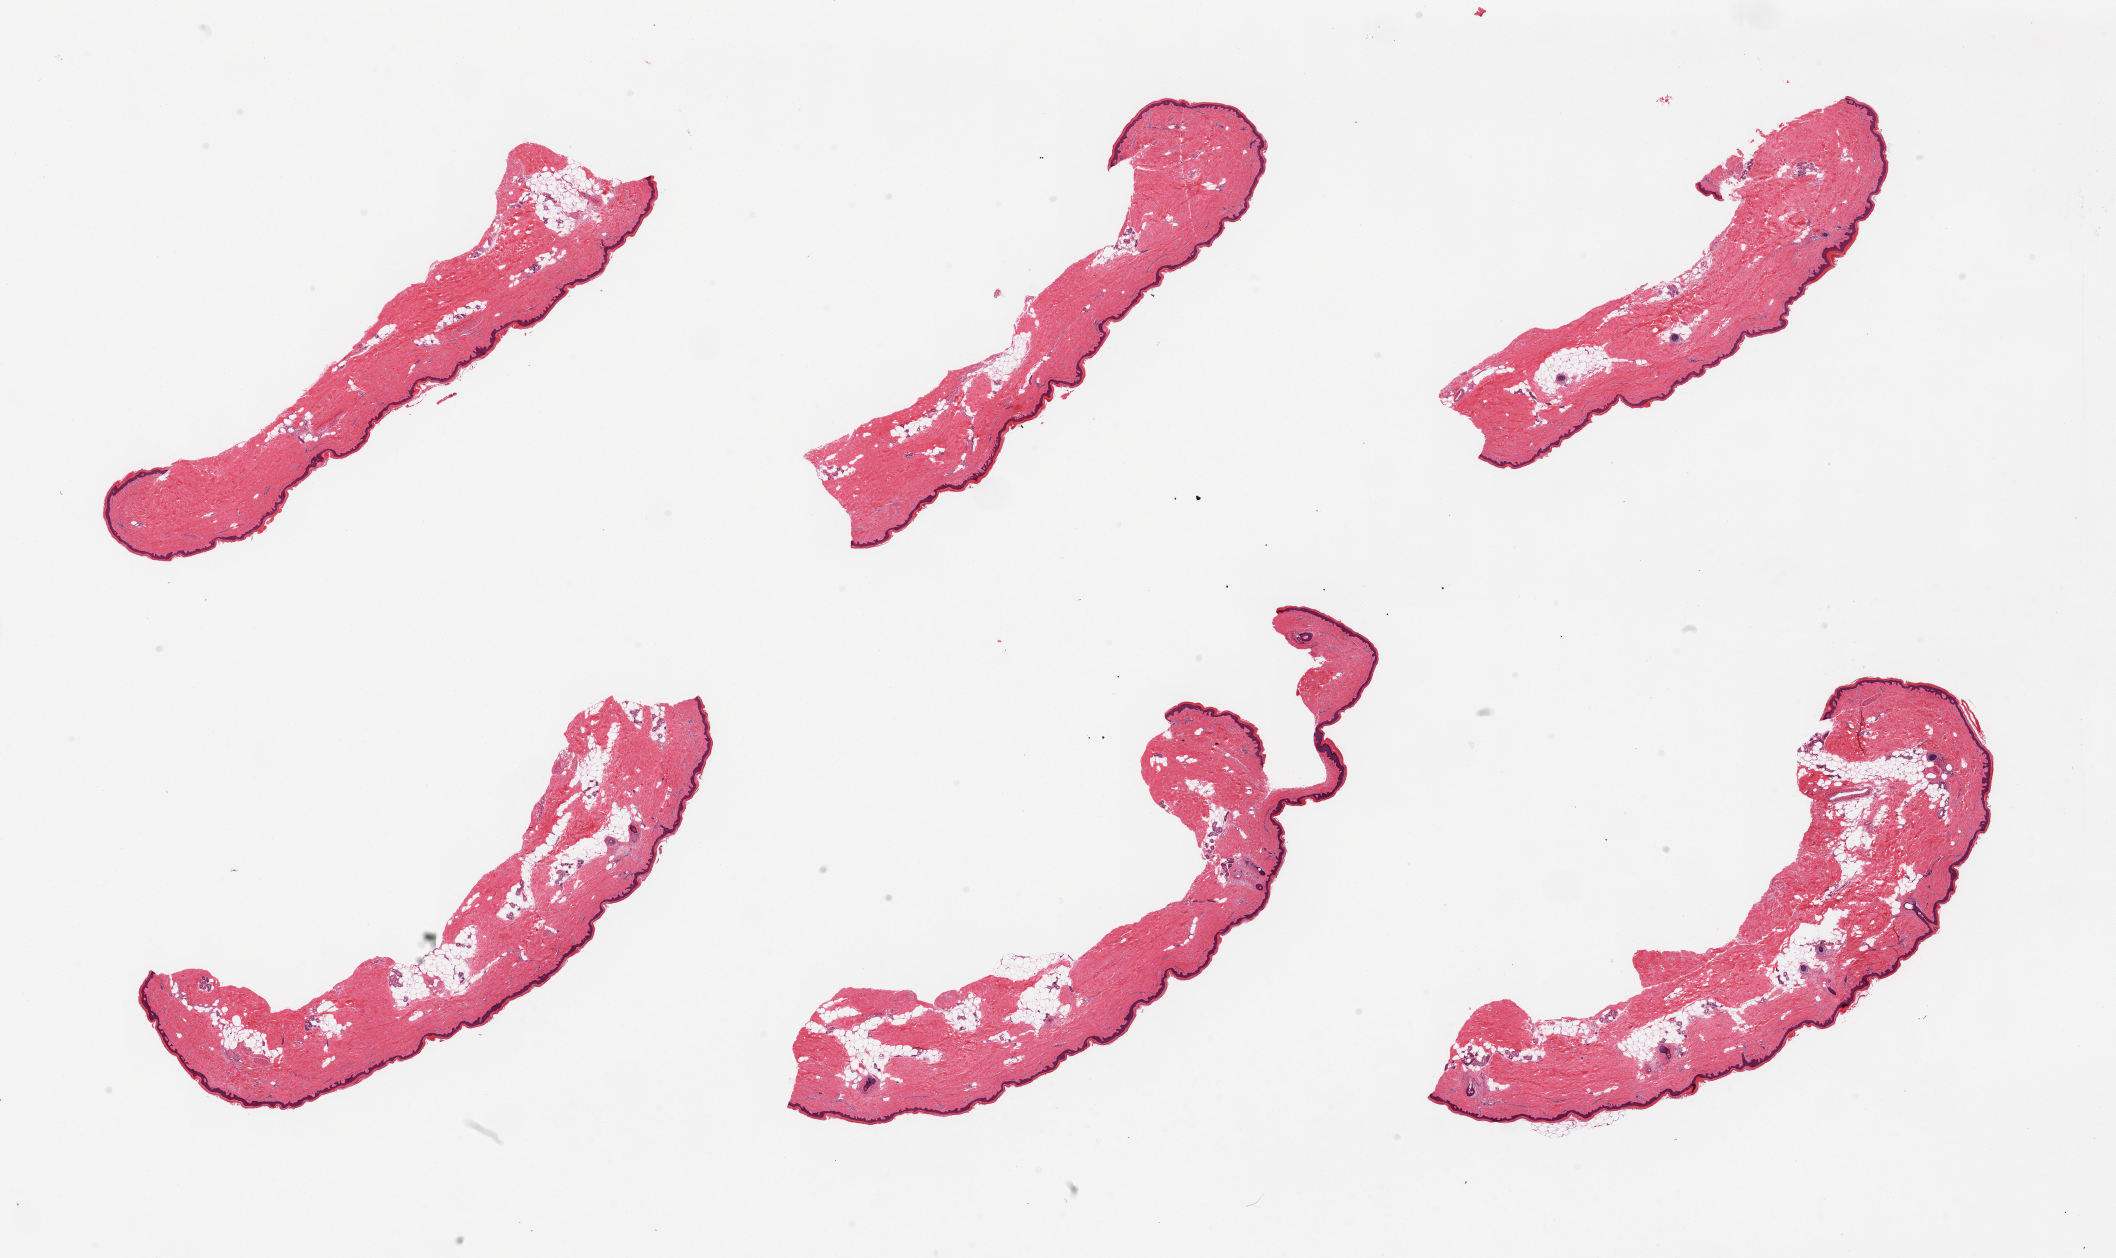
Hematoxylin and eosin (H&E) whole-slide image, whole scanned area (about 33.5 x 19.9 mm, acquisition: 20x scan) shown as a low-resolution overview, PAXgene-fixed, paraffin-embedded tissue, section of skin of lower leg (target tissue), tissue donor sample. Female donor.
Pathologist's review note for this sample: 6 pieces, well trimmed, but include up to 20% internal fat, squamous epithelium measures ~35 microns.